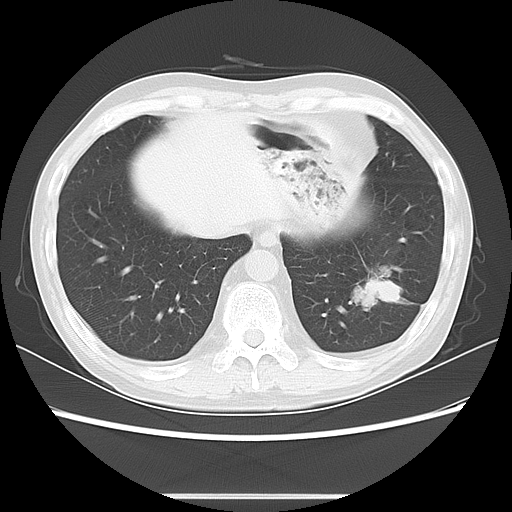
Chest CT, one axial slice. Slice 21 of 63 in the series (ordered by position). Reconstruction kernel LUNG. Lung window (W 1500 / L -600 HU). 512 × 512 image matrix. Male patient, age 49 years. Case-level facts recorded for this patient, not image findings: clinical TNM (as recorded): T3 N0 M0; histopathological grade: G2-3.
Outlined on this slice (rectangle marked by the reading radiologist):
- lung tumour (recorded histology: squamous cell carcinoma): bounding box (x1, y1, x2, y2) in pixels: (348, 262, 407, 316)